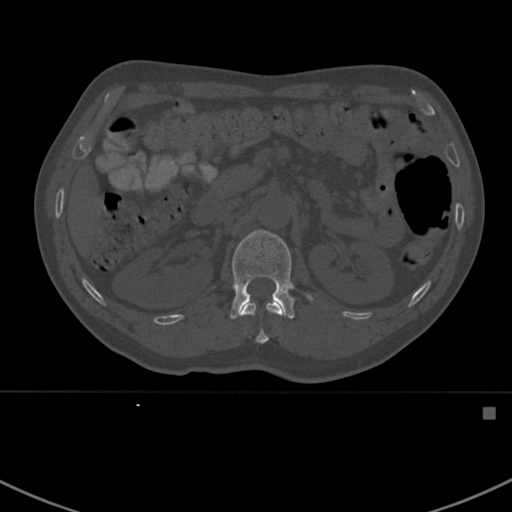
CT including the spine, one axial slice; slice 315 of 412 in the series (ordered by position); reconstruction kernel Br40s; 120 kVp; bone window (W 1800 / L 400 HU); 1.5 mm slice thickness; 512 × 512 image matrix, field of view 358 × 358 mm. Male patient, age 59 years. From the clinical record (not read from this slice): primary cancer: prostate.
Annotated regions visible in this slice (semi-automatic segmentation, software-assisted and operator-edited):
- L1 vertebra: bounding box [x1, y1, x2, y2] px = [230, 230, 314, 319]
- T12 vertebra: [242, 303, 281, 344]